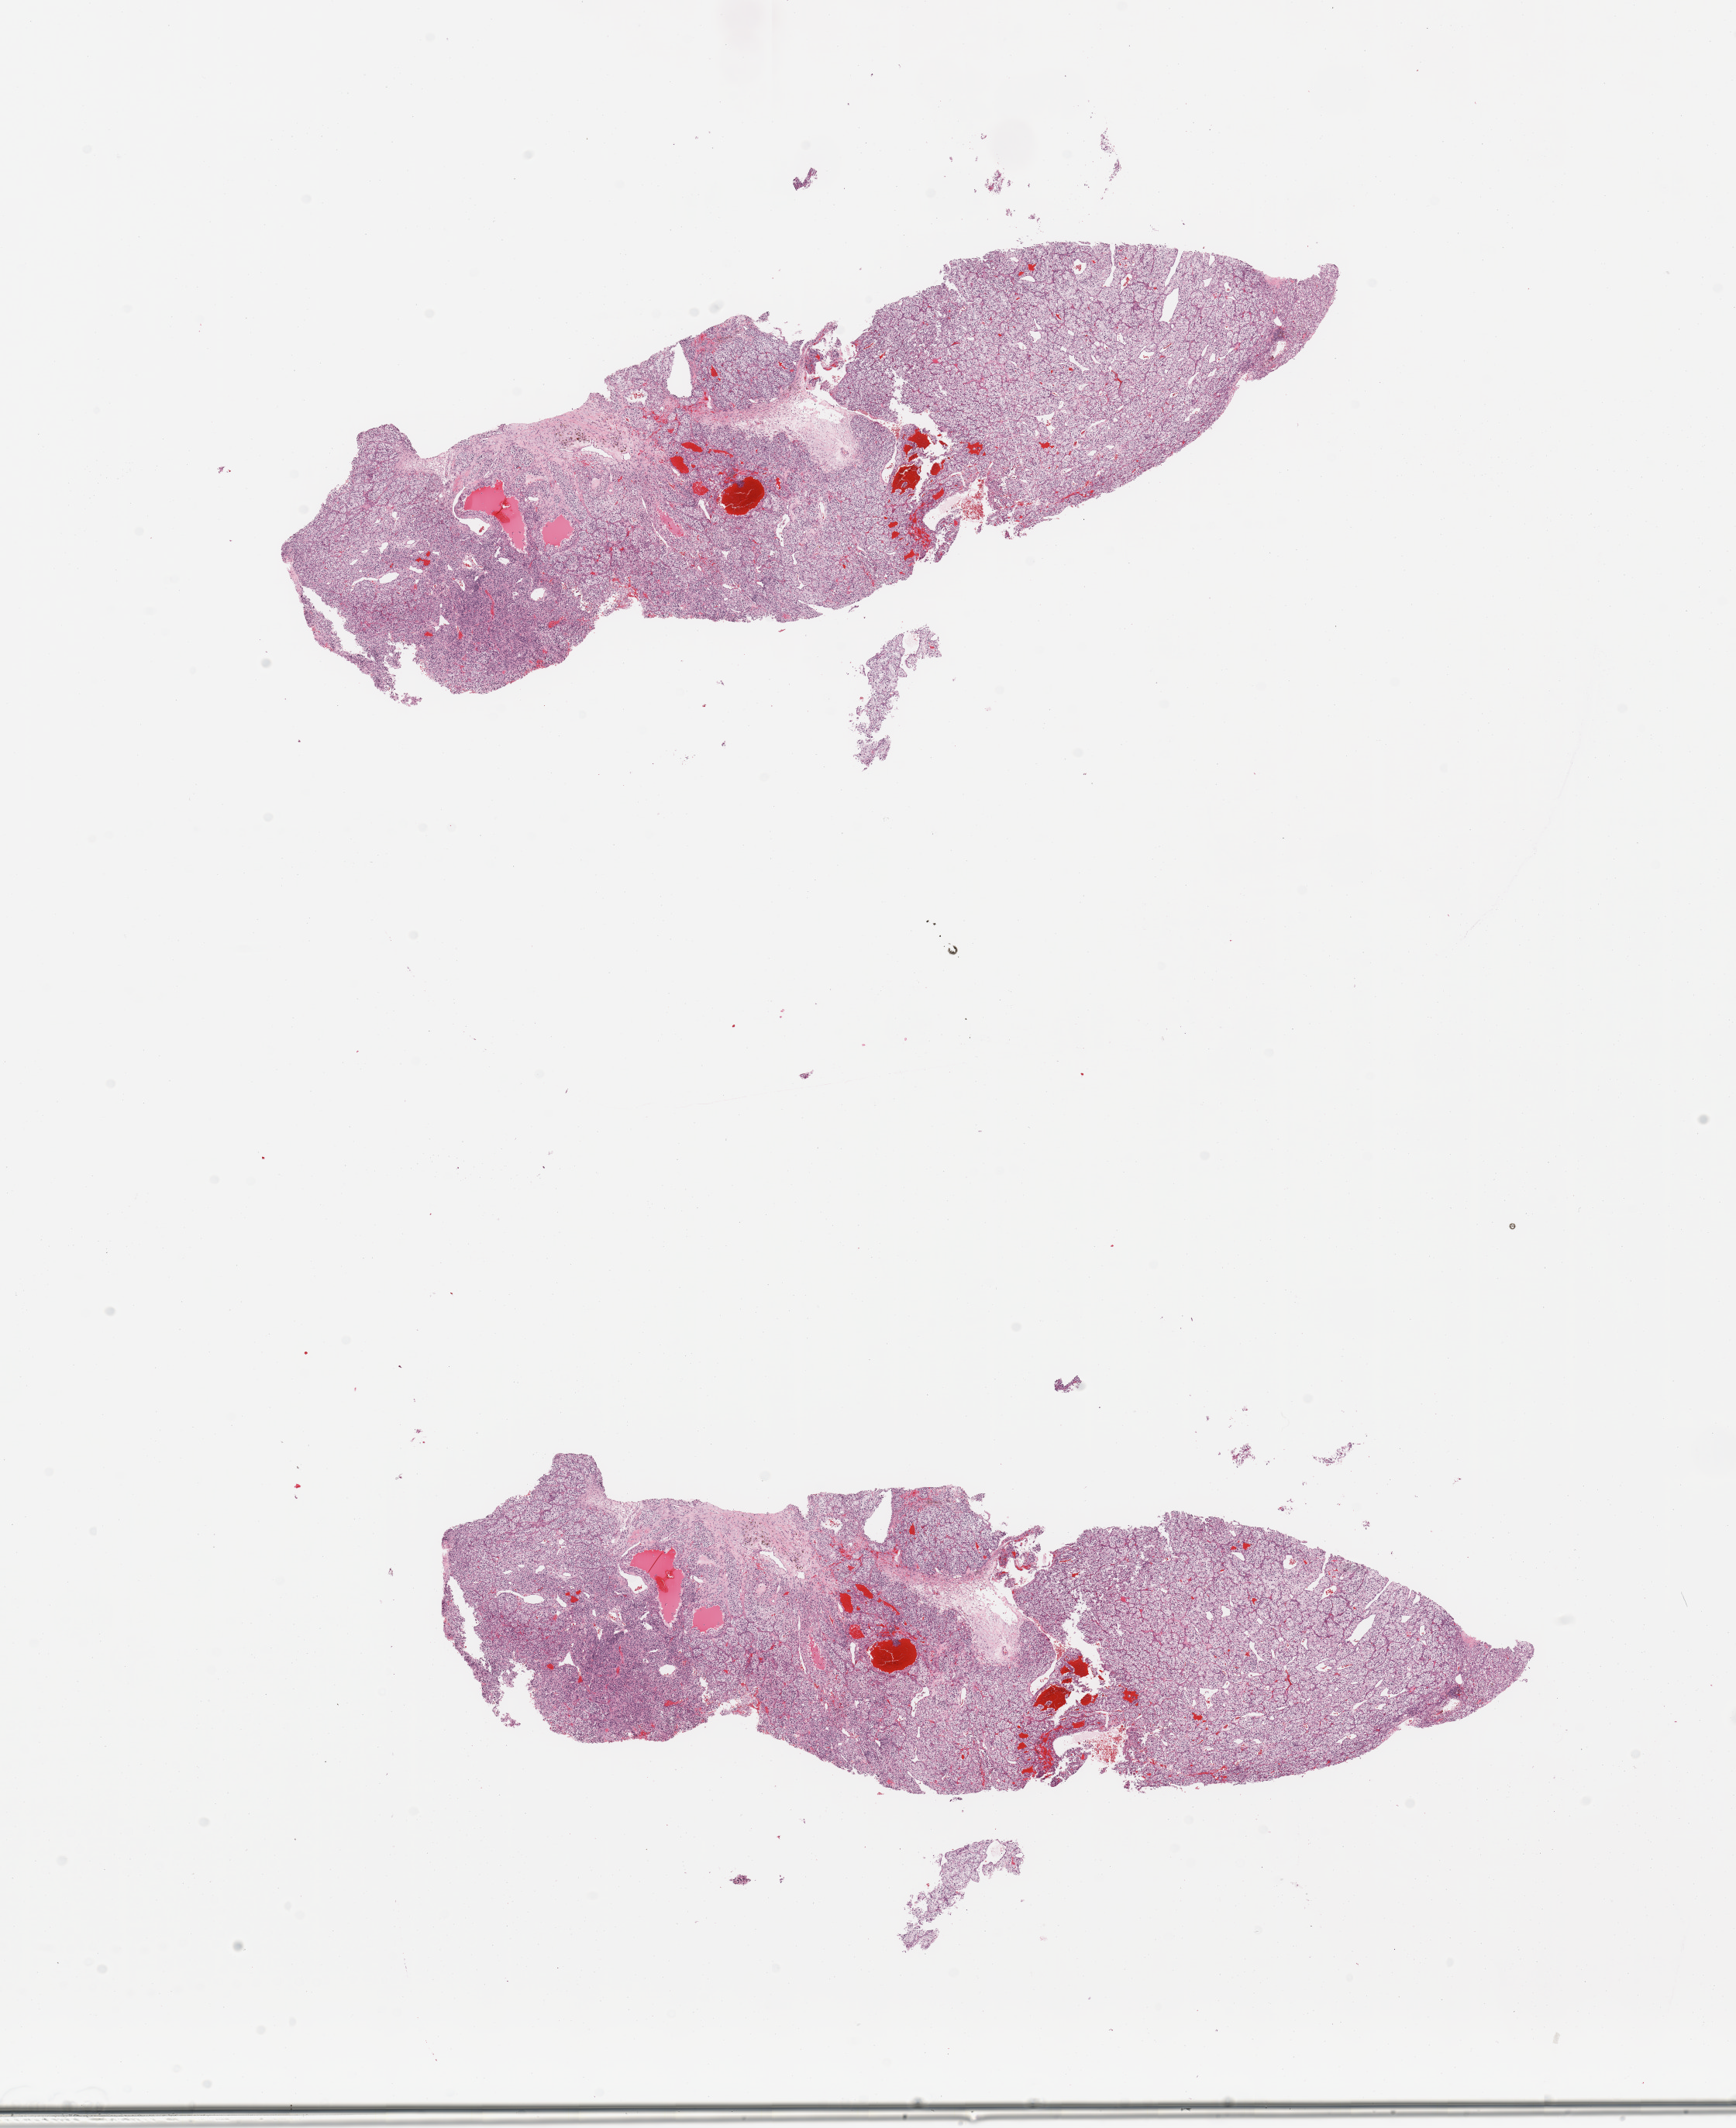
Digitized H&E-stained tissue section (whole slide) — shown as a low-resolution overview of the whole scanned area (about 17.7 x 21.7 mm). Tumour tissue sample, sampled site: kidney. Patient: male, age 83 years. Histologic grade: G3 (poorly differentiated). Slide review estimates, as recorded: tumour nuclei 90%, necrosis 5%.
- primary tumour site (as recorded): lower pole
- diagnosis: Renal cell carcinoma, NOS
- AJCC pathologic stage: III